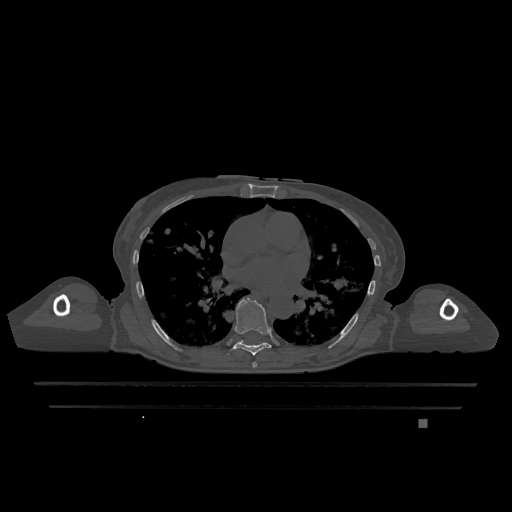
CT including the spine, one axial slice; slice 734 of 1317 in the series (ordered by position); bone window (W 1800 / L 400 HU); 0.5 mm slice thickness; 512 × 512 image matrix, field of view 500 × 500 mm. Patient: female, 74 years. From the clinical record (not read from this slice): primary cancer: lung; vertebrae with lytic lesions (as recorded): T1, T4, T5, T6, L4, L5.
Annotated regions visible in this slice (semi-automatic segmentation, software-assisted and operator-edited):
- T6 vertebra: bounding box <252,362,257,368> (left, top, right, bottom; pixels)
- T7 vertebra: <232,298,271,355>